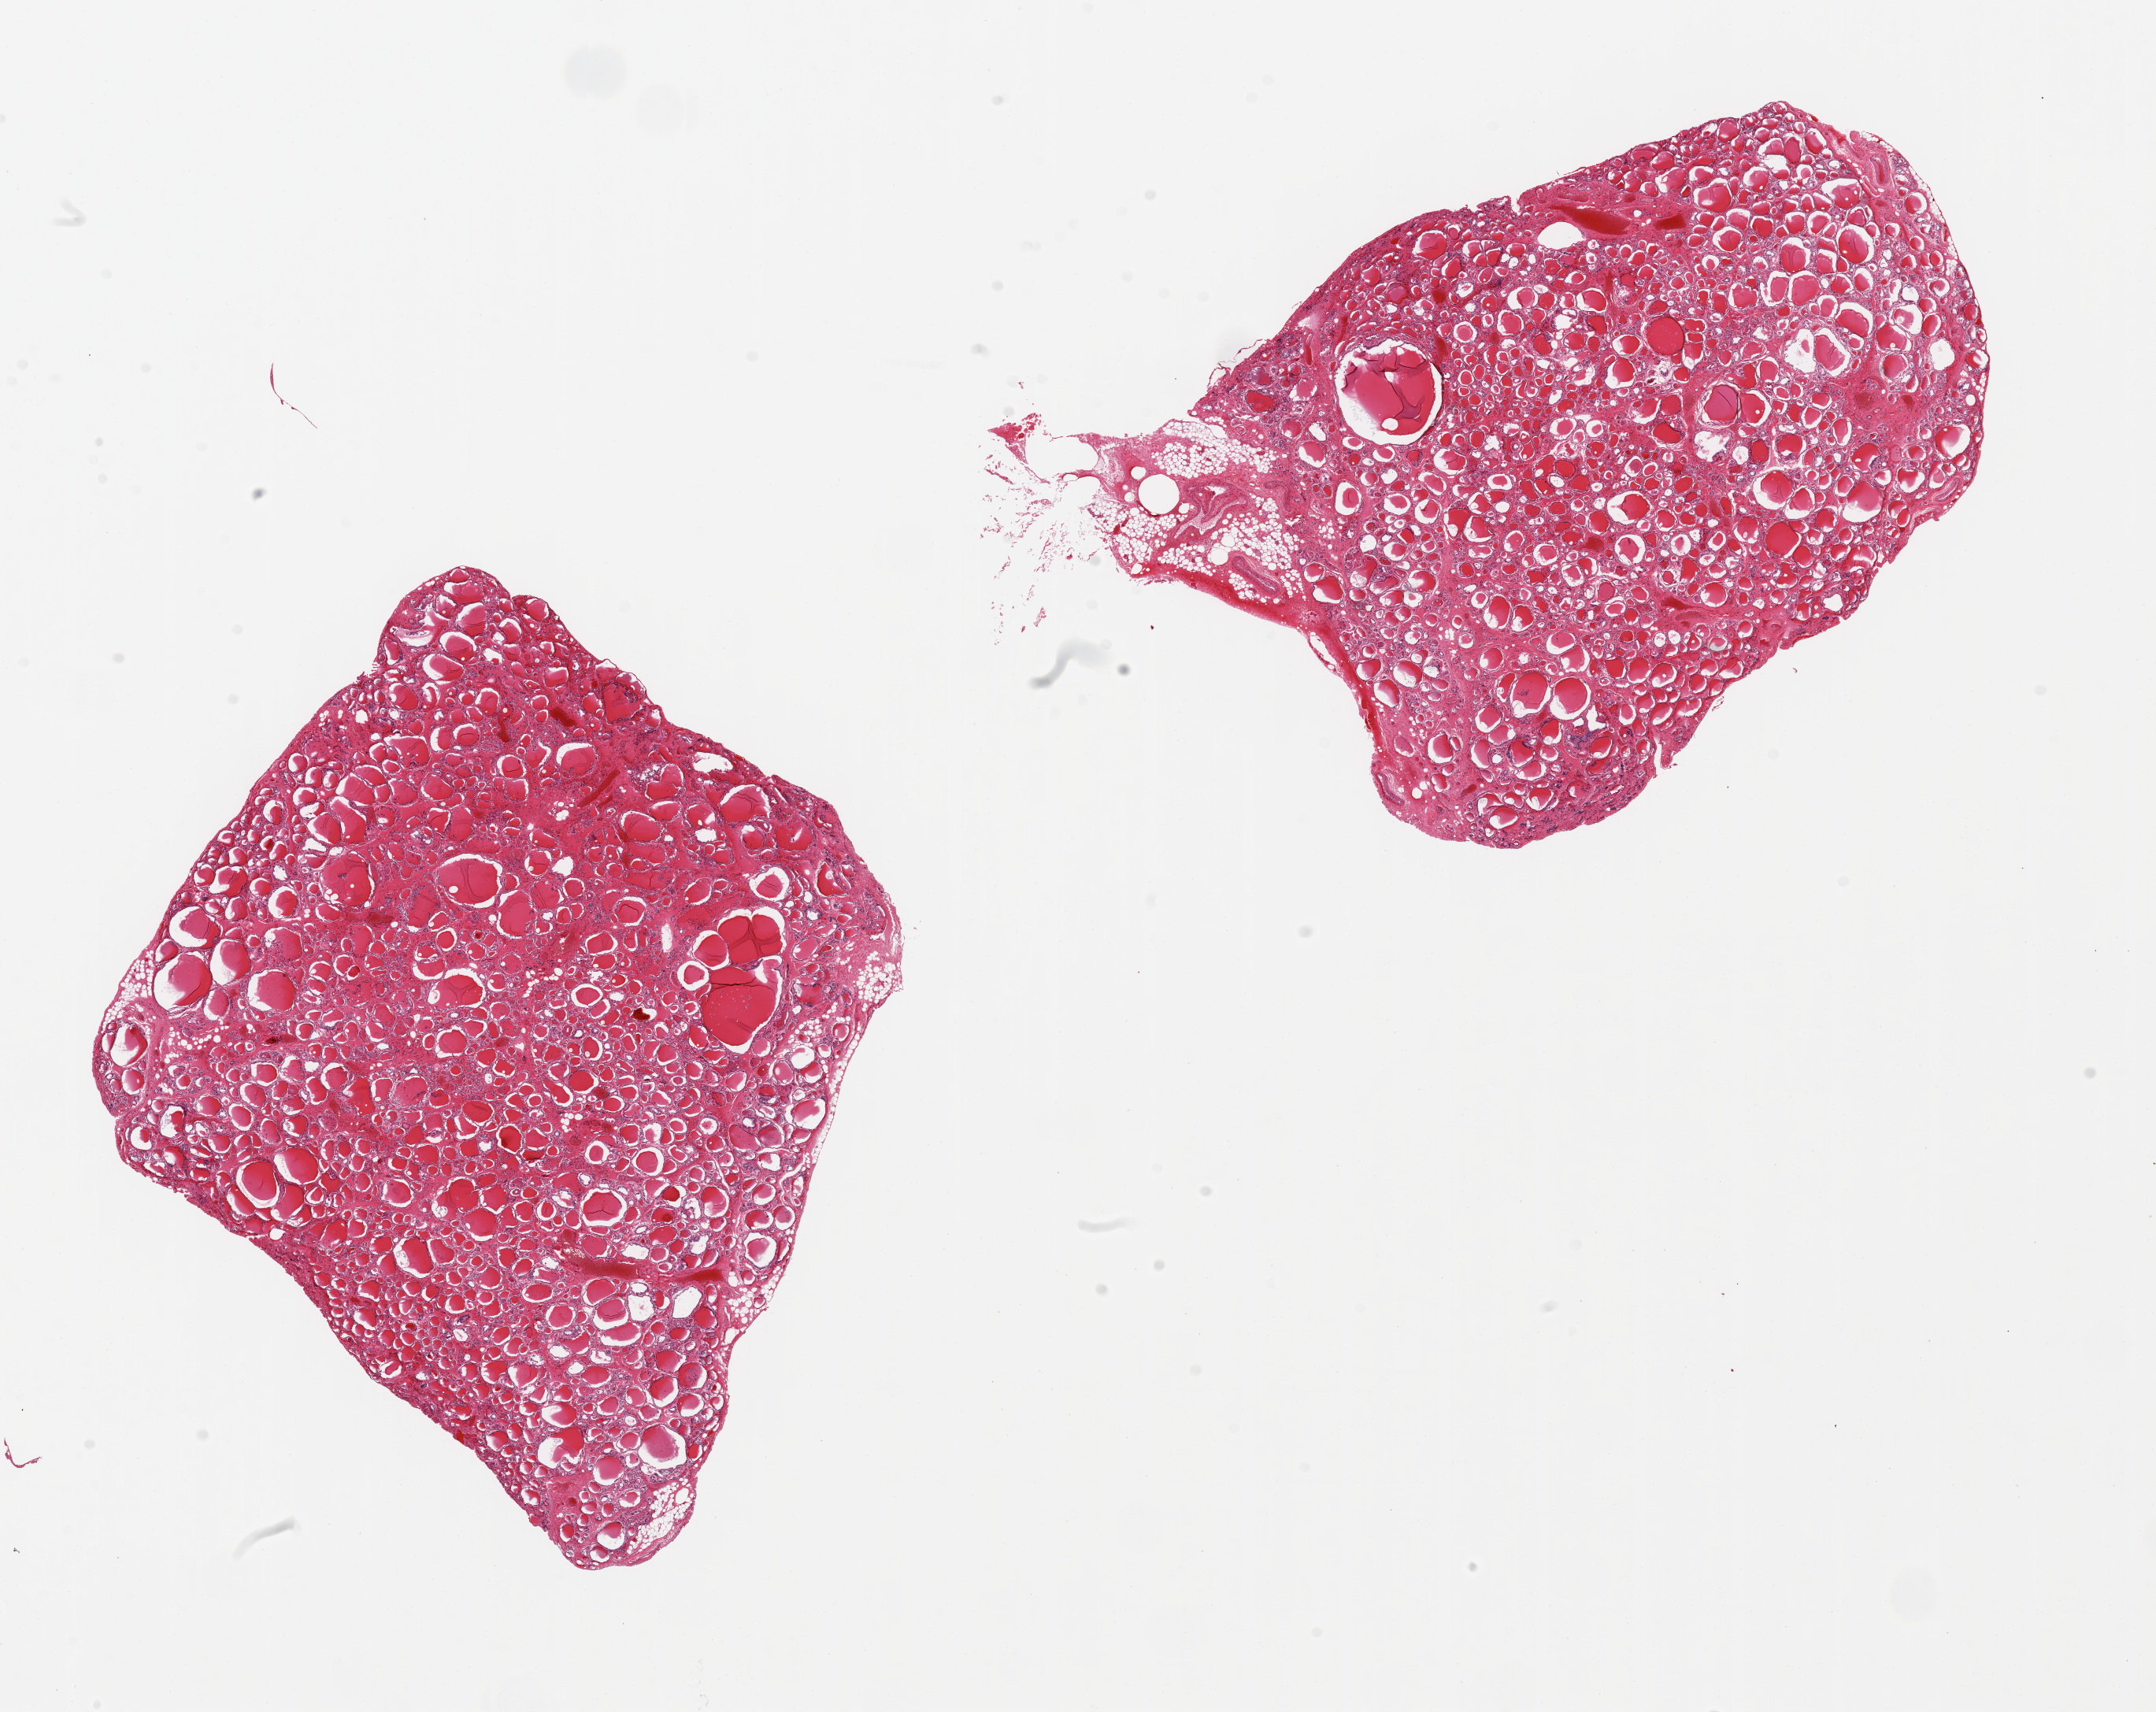
Haematoxylin and eosin whole-slide image, shown as a low-resolution overview of the whole scanned area (about 21.7 x 17.2 mm), PAXgene-fixed, paraffin-embedded tissue, sampled site (target tissue): thyroid, tissue donor sample. Male donor.
- pathologist's review note for this sample: 2 pieces ~7x6mms, few colloid cysts ~1 mm d